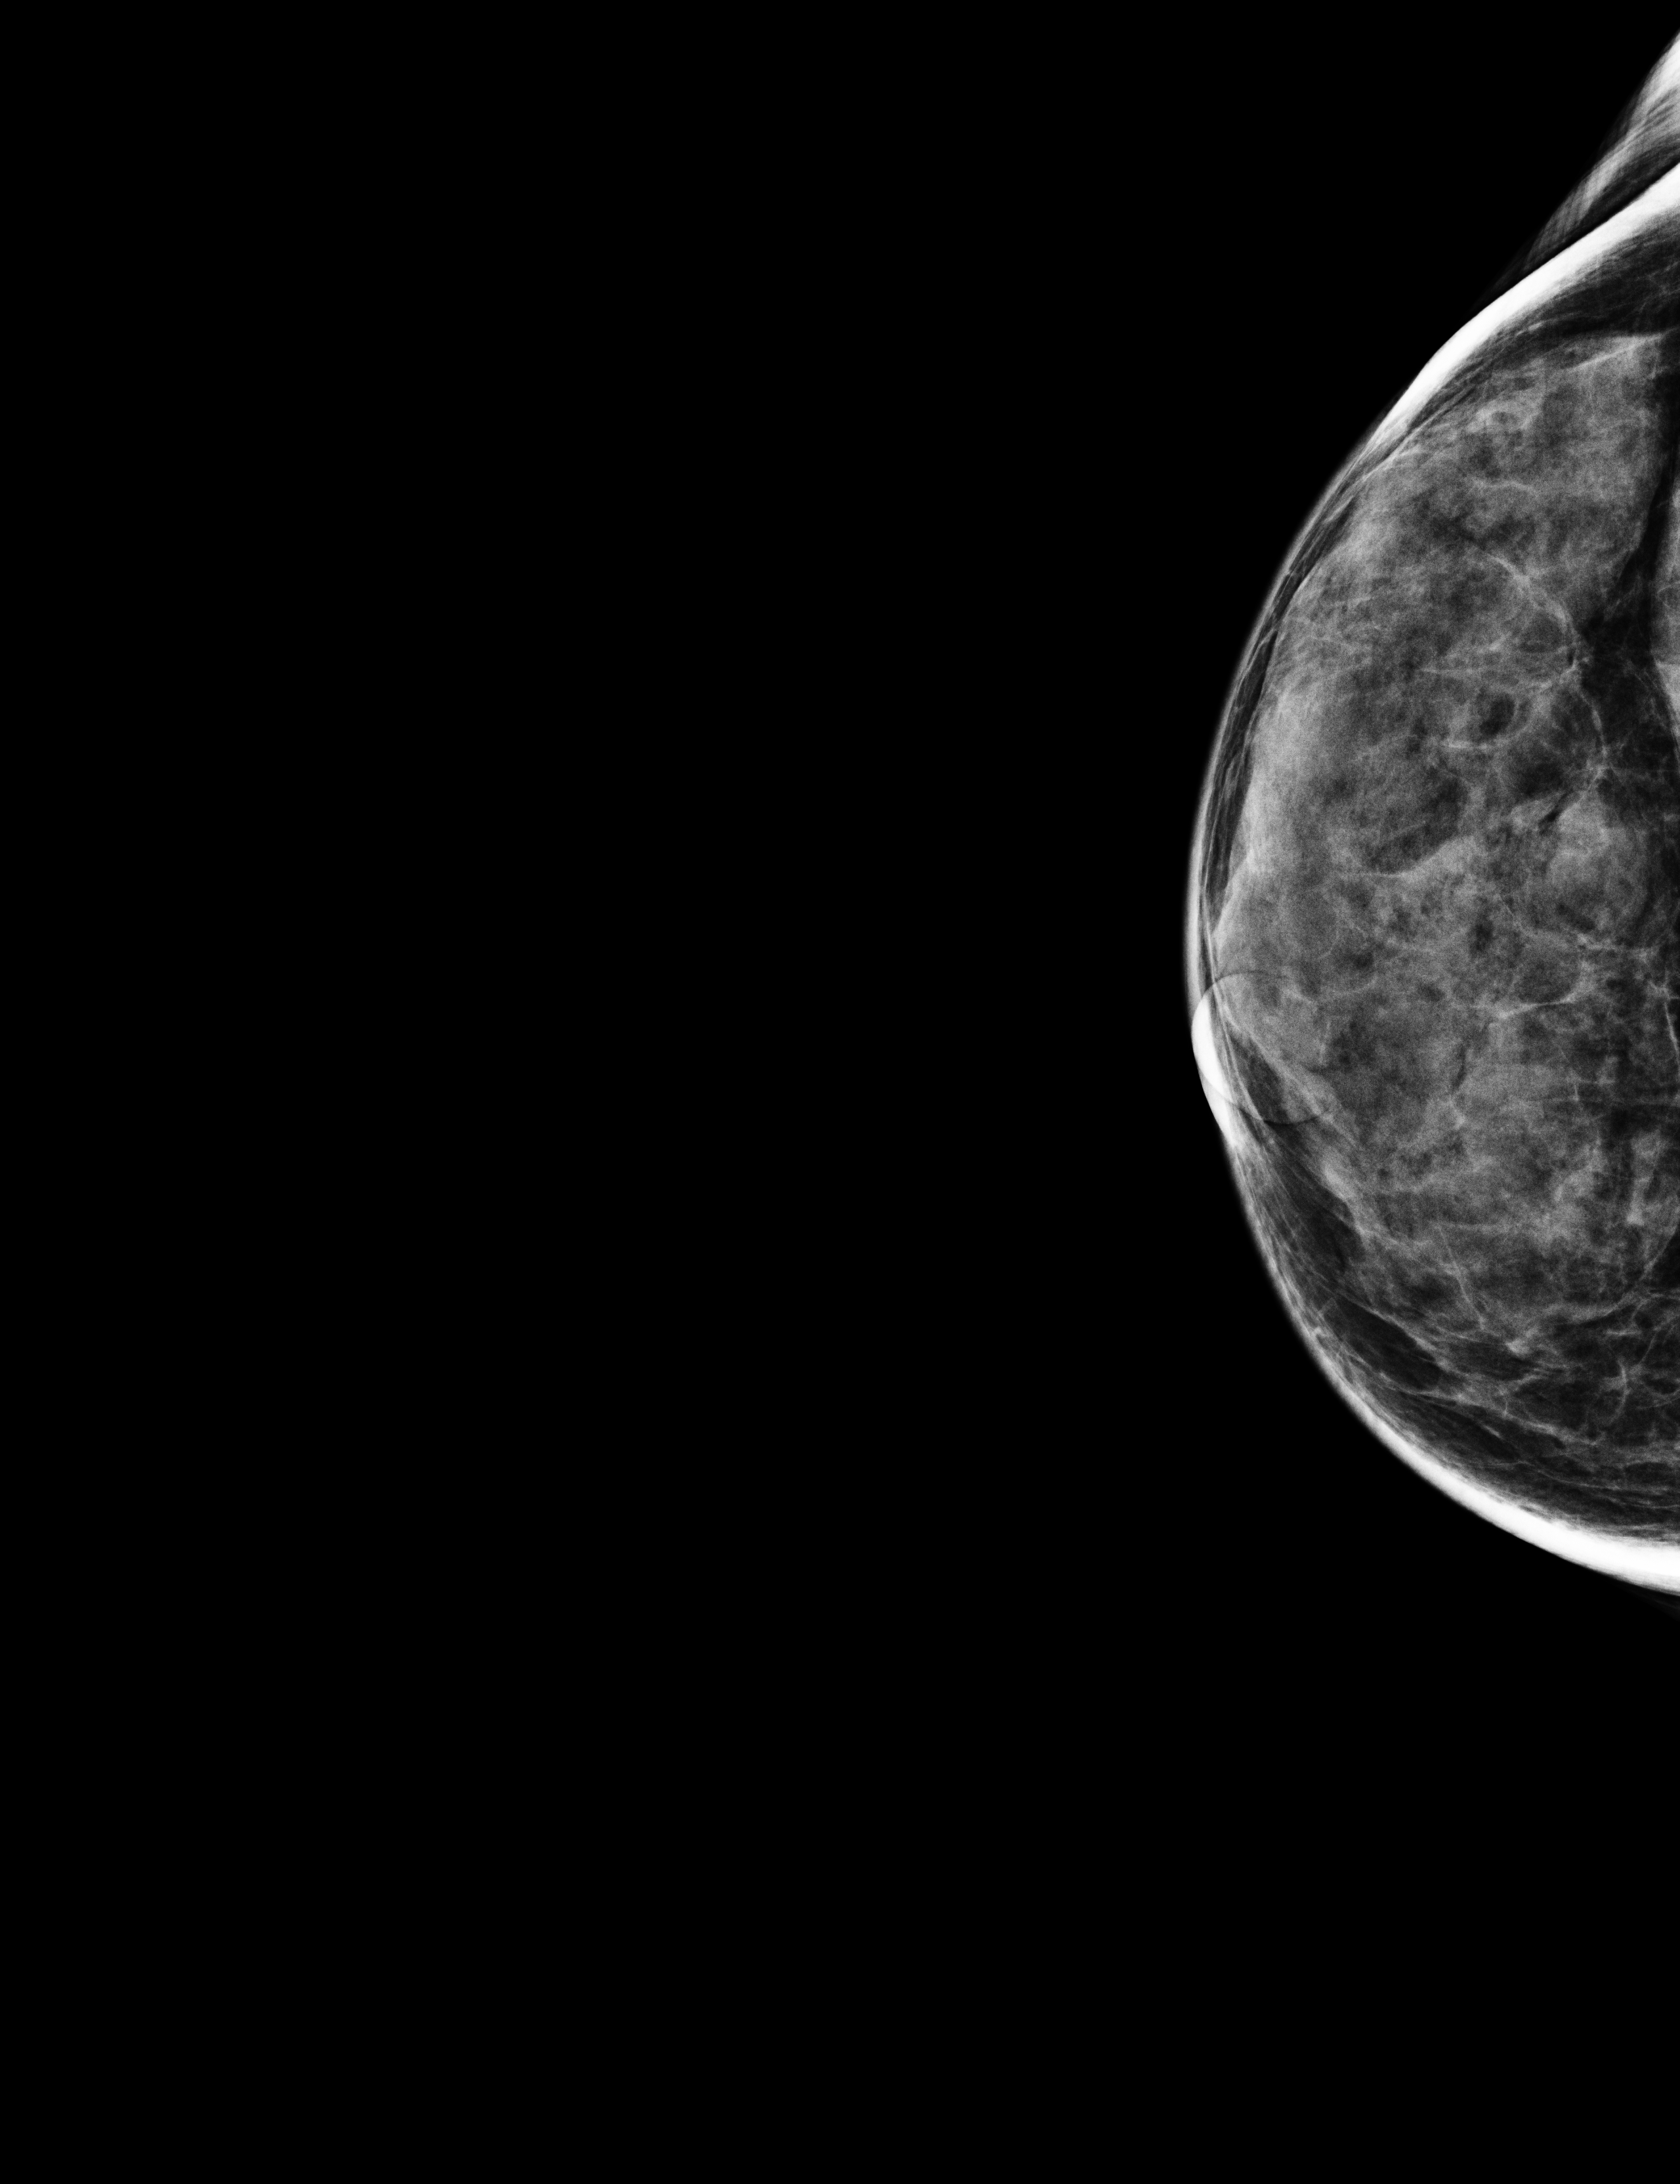
Screening examination; compressed breast thickness 27 mm; system: Selenia Dimensions. Female patient, age 44 years.
Image type: full-field digital mammogram. Breast: right. Projection: craniocaudal (CC) view.